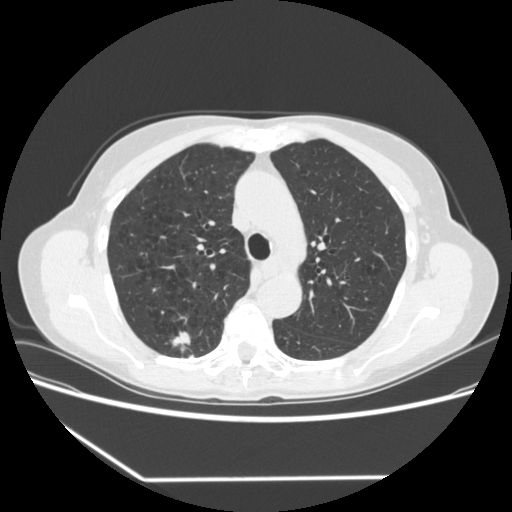
Chest CT (low-dose screening protocol), one axial image; baseline screening round; lung window (W 1500 / L -600 HU); 1.25 mm slice thickness. Female, age 67 years at enrolment. Current smoker at enrolment.
Expert-annotated lung lesion, box from (x=158, y=324) to (x=201, y=362) px. The screening reader recorded 2 non-calcified nodules or masses ≥4 mm on this exam (right upper lobe, right lower lobe); which of them this box marks is not recorded. Official screen result: positive, change unspecified: nodule(s) >= 4 mm or enlarging nodule(s), mass(es), or other non-specific abnormalities suspicious for lung cancer.